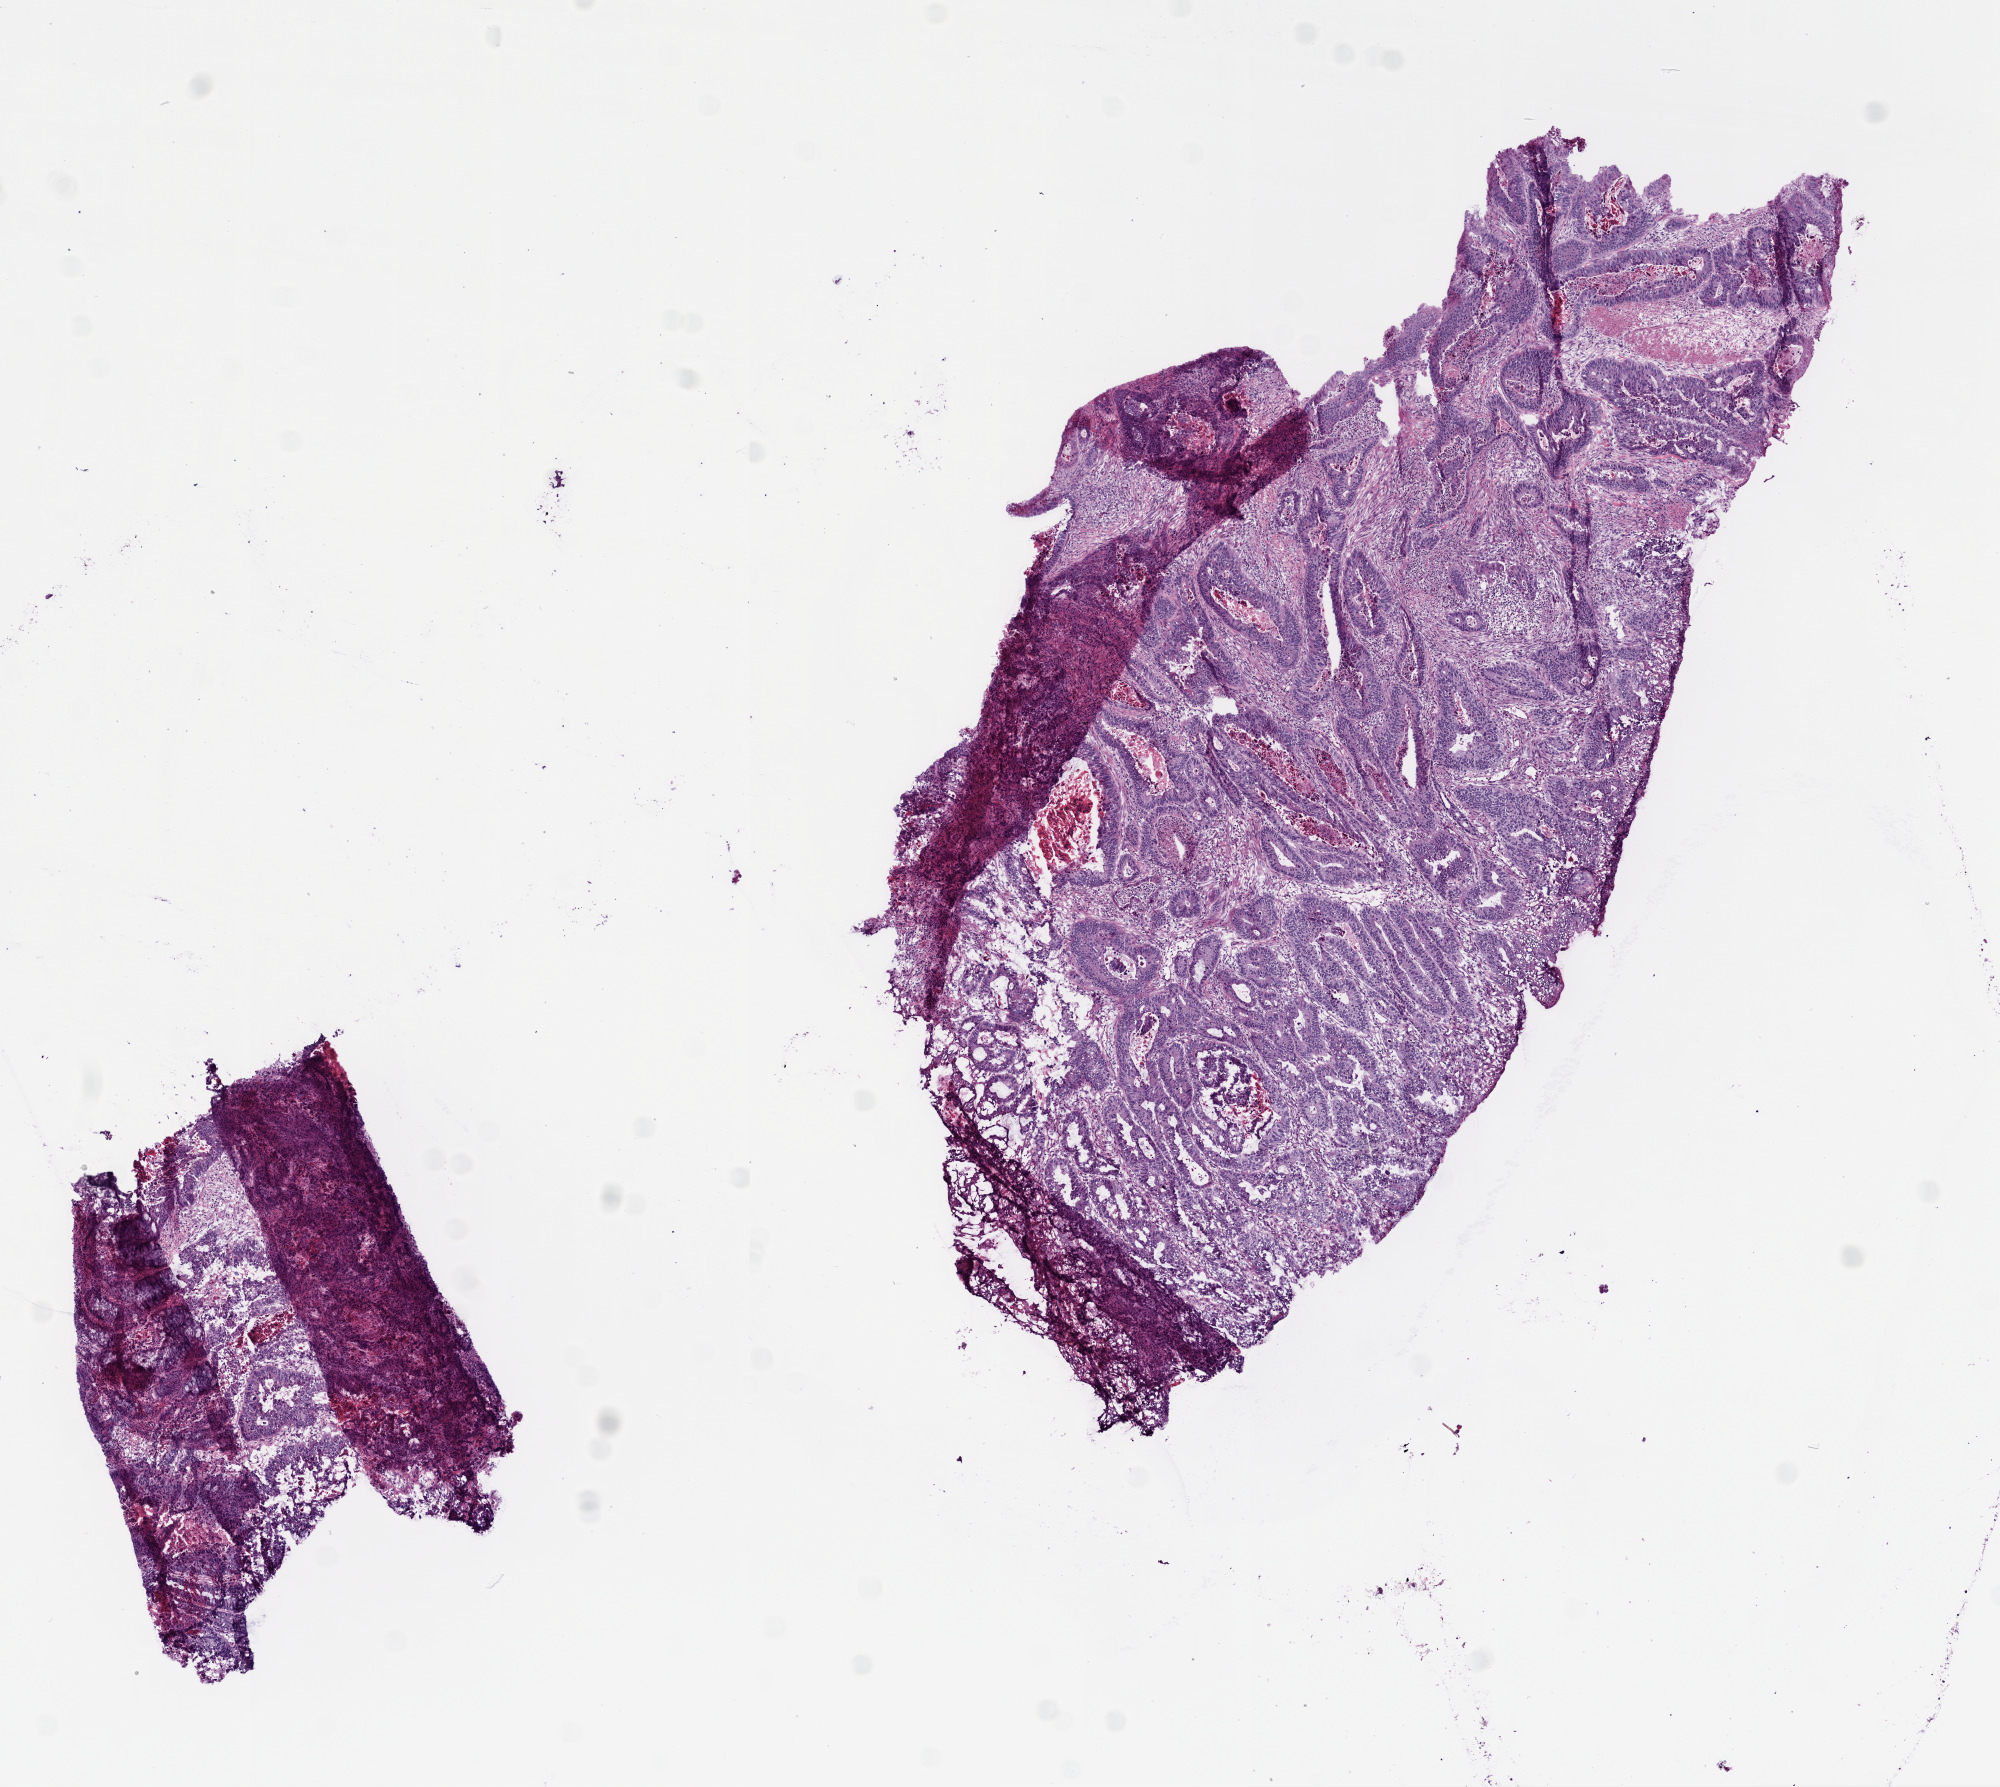
Hematoxylin and eosin (H&E) stained whole-slide image — low-resolution overview of the scanned area, about 8.0 x 7.2 mm (slide scanned at 20x), frozen section, primary tumour sample from the colon. Male, age 64 years at initial diagnosis. Composition of this section per pathologist review: tumour cells 75%, tumour nuclei 65%, normal cells 0%, stromal cells 10%, necrosis 15%.
Diagnosis: Adenocarcinoma, NOS. AJCC pathologic stage: II (5th edition).